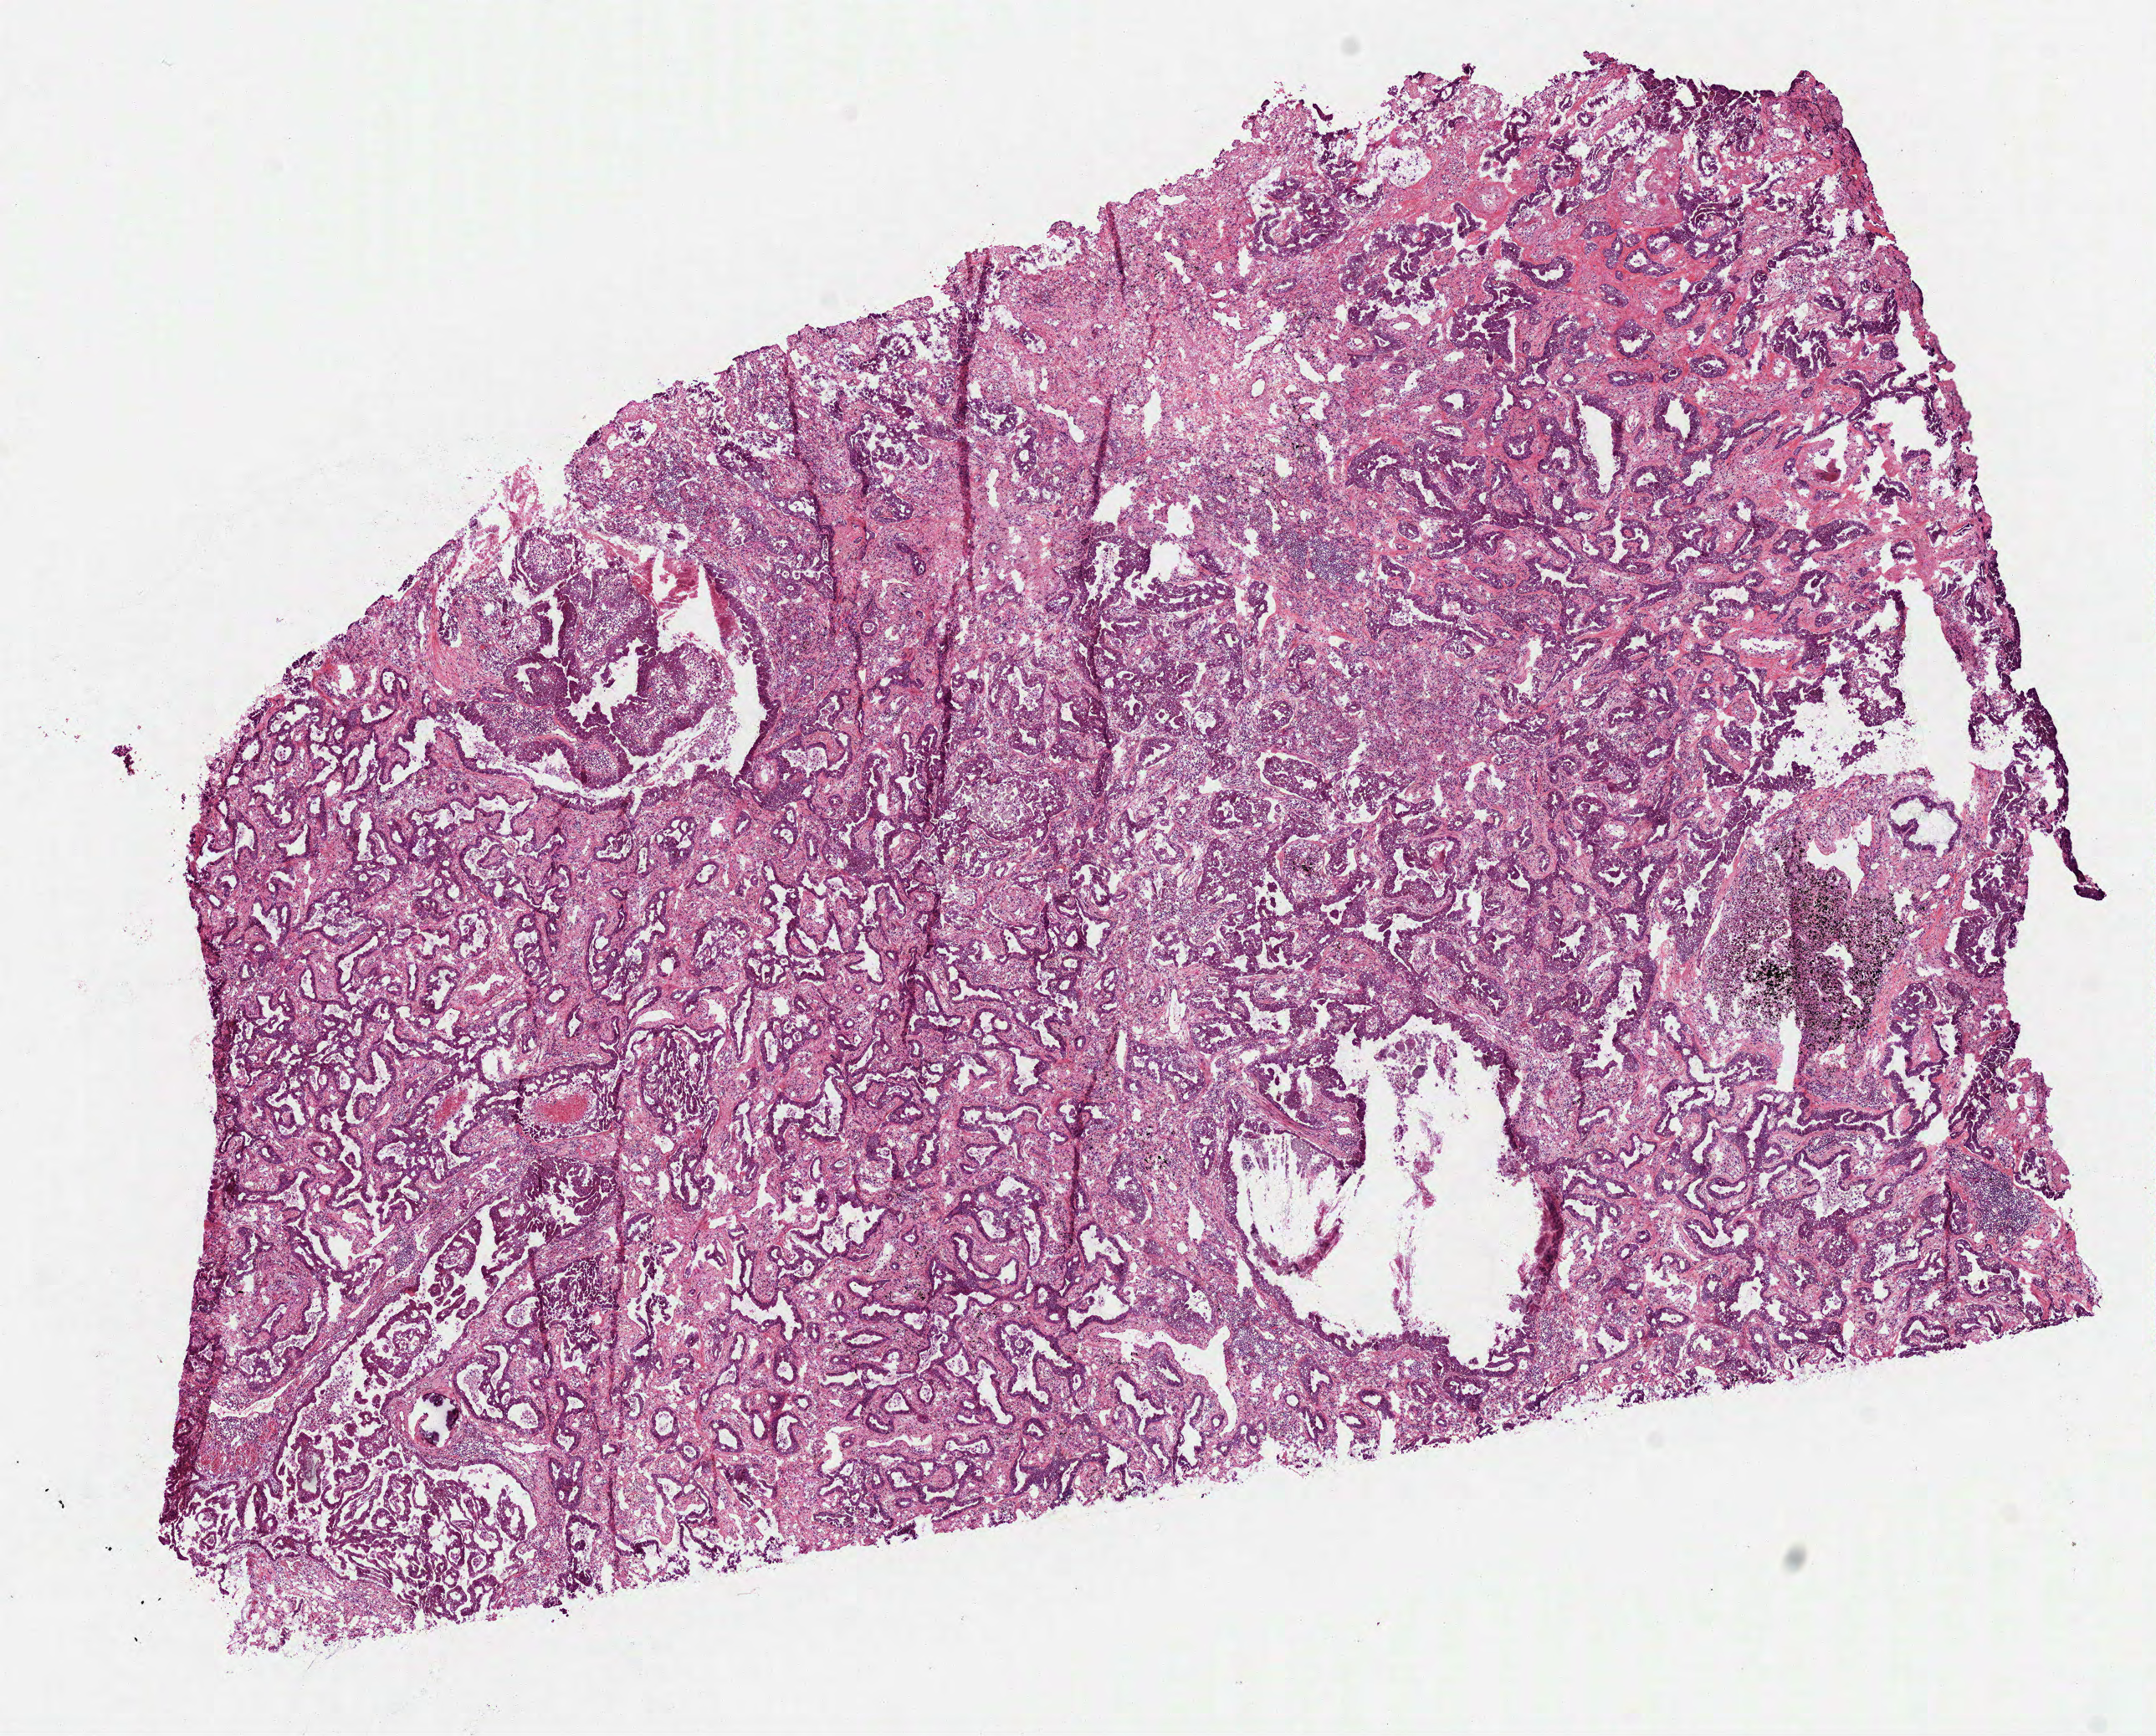
H&E-stained whole-slide image — low-resolution overview of the scanned area, about 10.4 x 8.4 mm (from a 40x scan). Frozen section from the bottom of the tissue portion. Primary tumour sample from the lung. Female, age 65 years at initial diagnosis. Pathologist review of this section (percent, as recorded): tumour cells 80%, tumour nuclei 60%, normal cells 0%, stromal cells 15%, necrosis 5%.
- histologic diagnosis: Adenocarcinoma with mixed subtypes (overlapping lesion of lung)
- TNM: T2 N0 M0
- AJCC pathologic stage: IB (6th edition)